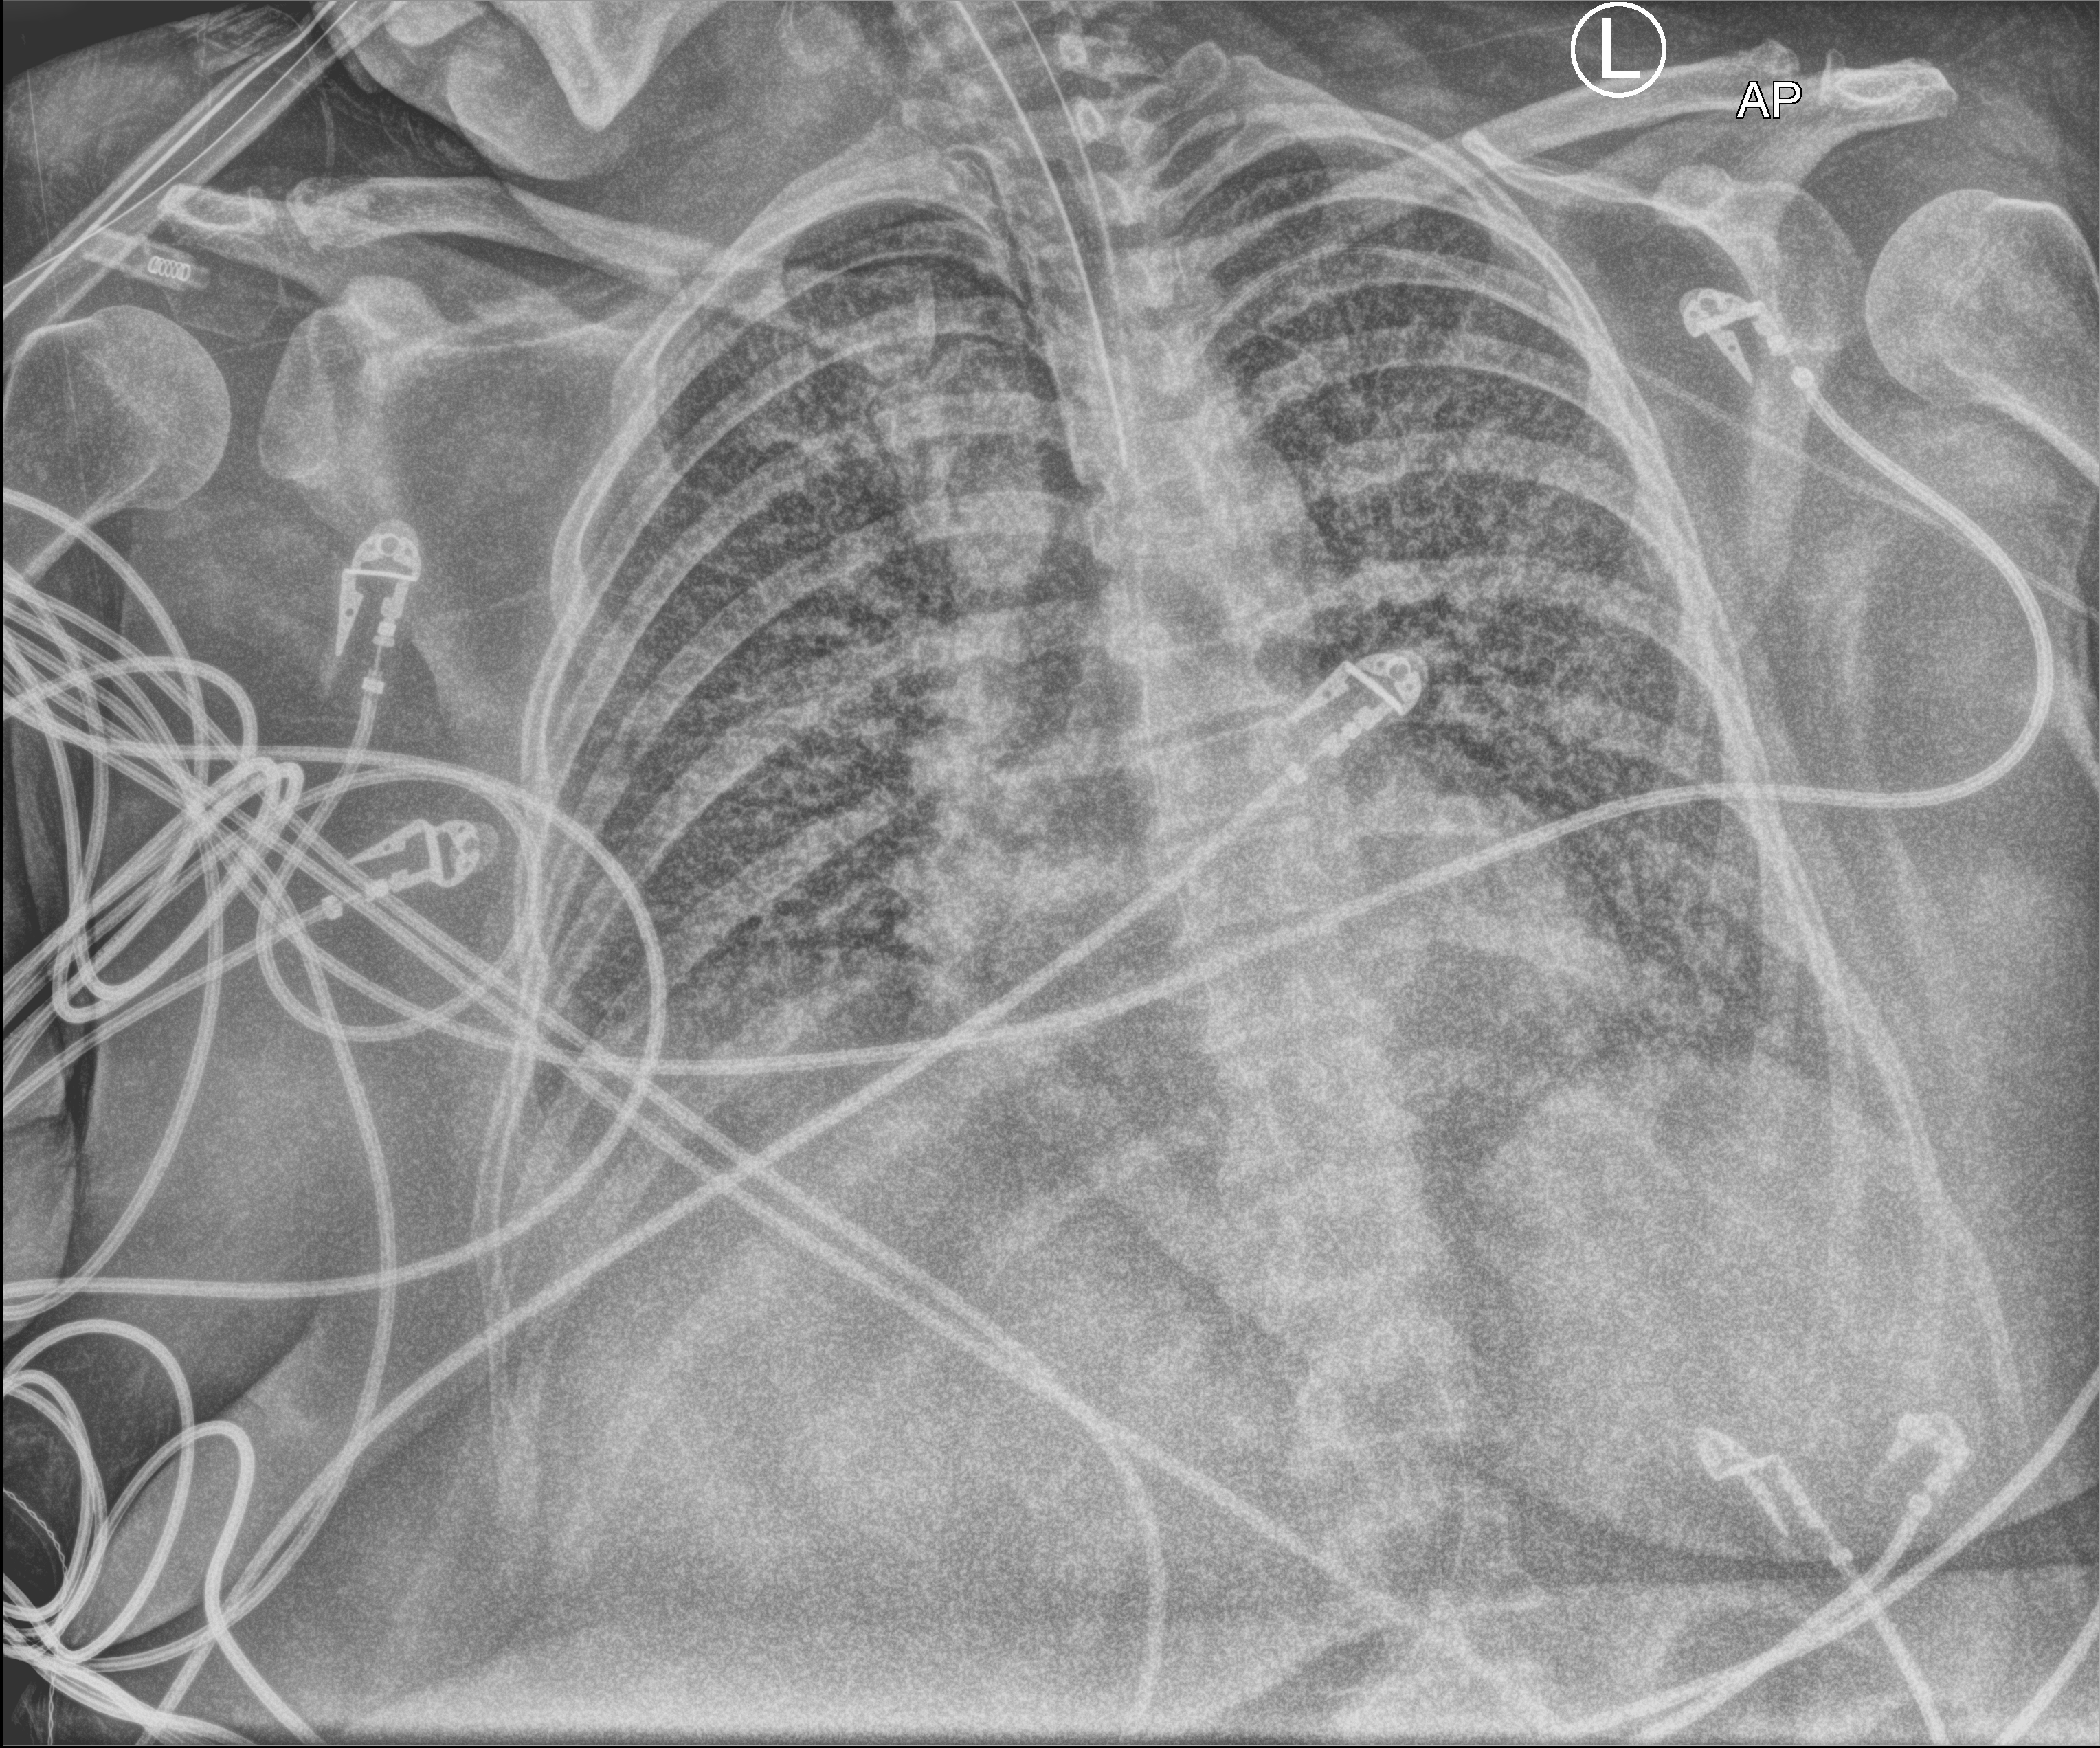
Portable chest radiograph, anteroposterior (AP) projection. Patient hospitalised with COVID-19; female, aged 18–59 years.
Hospital-stay facts (about this admission, not read from this image; timing relative to this image not recorded):
- length of hospital stay: 95 days
- mechanically ventilated during this hospital stay: yes
- COPD (admission record): no